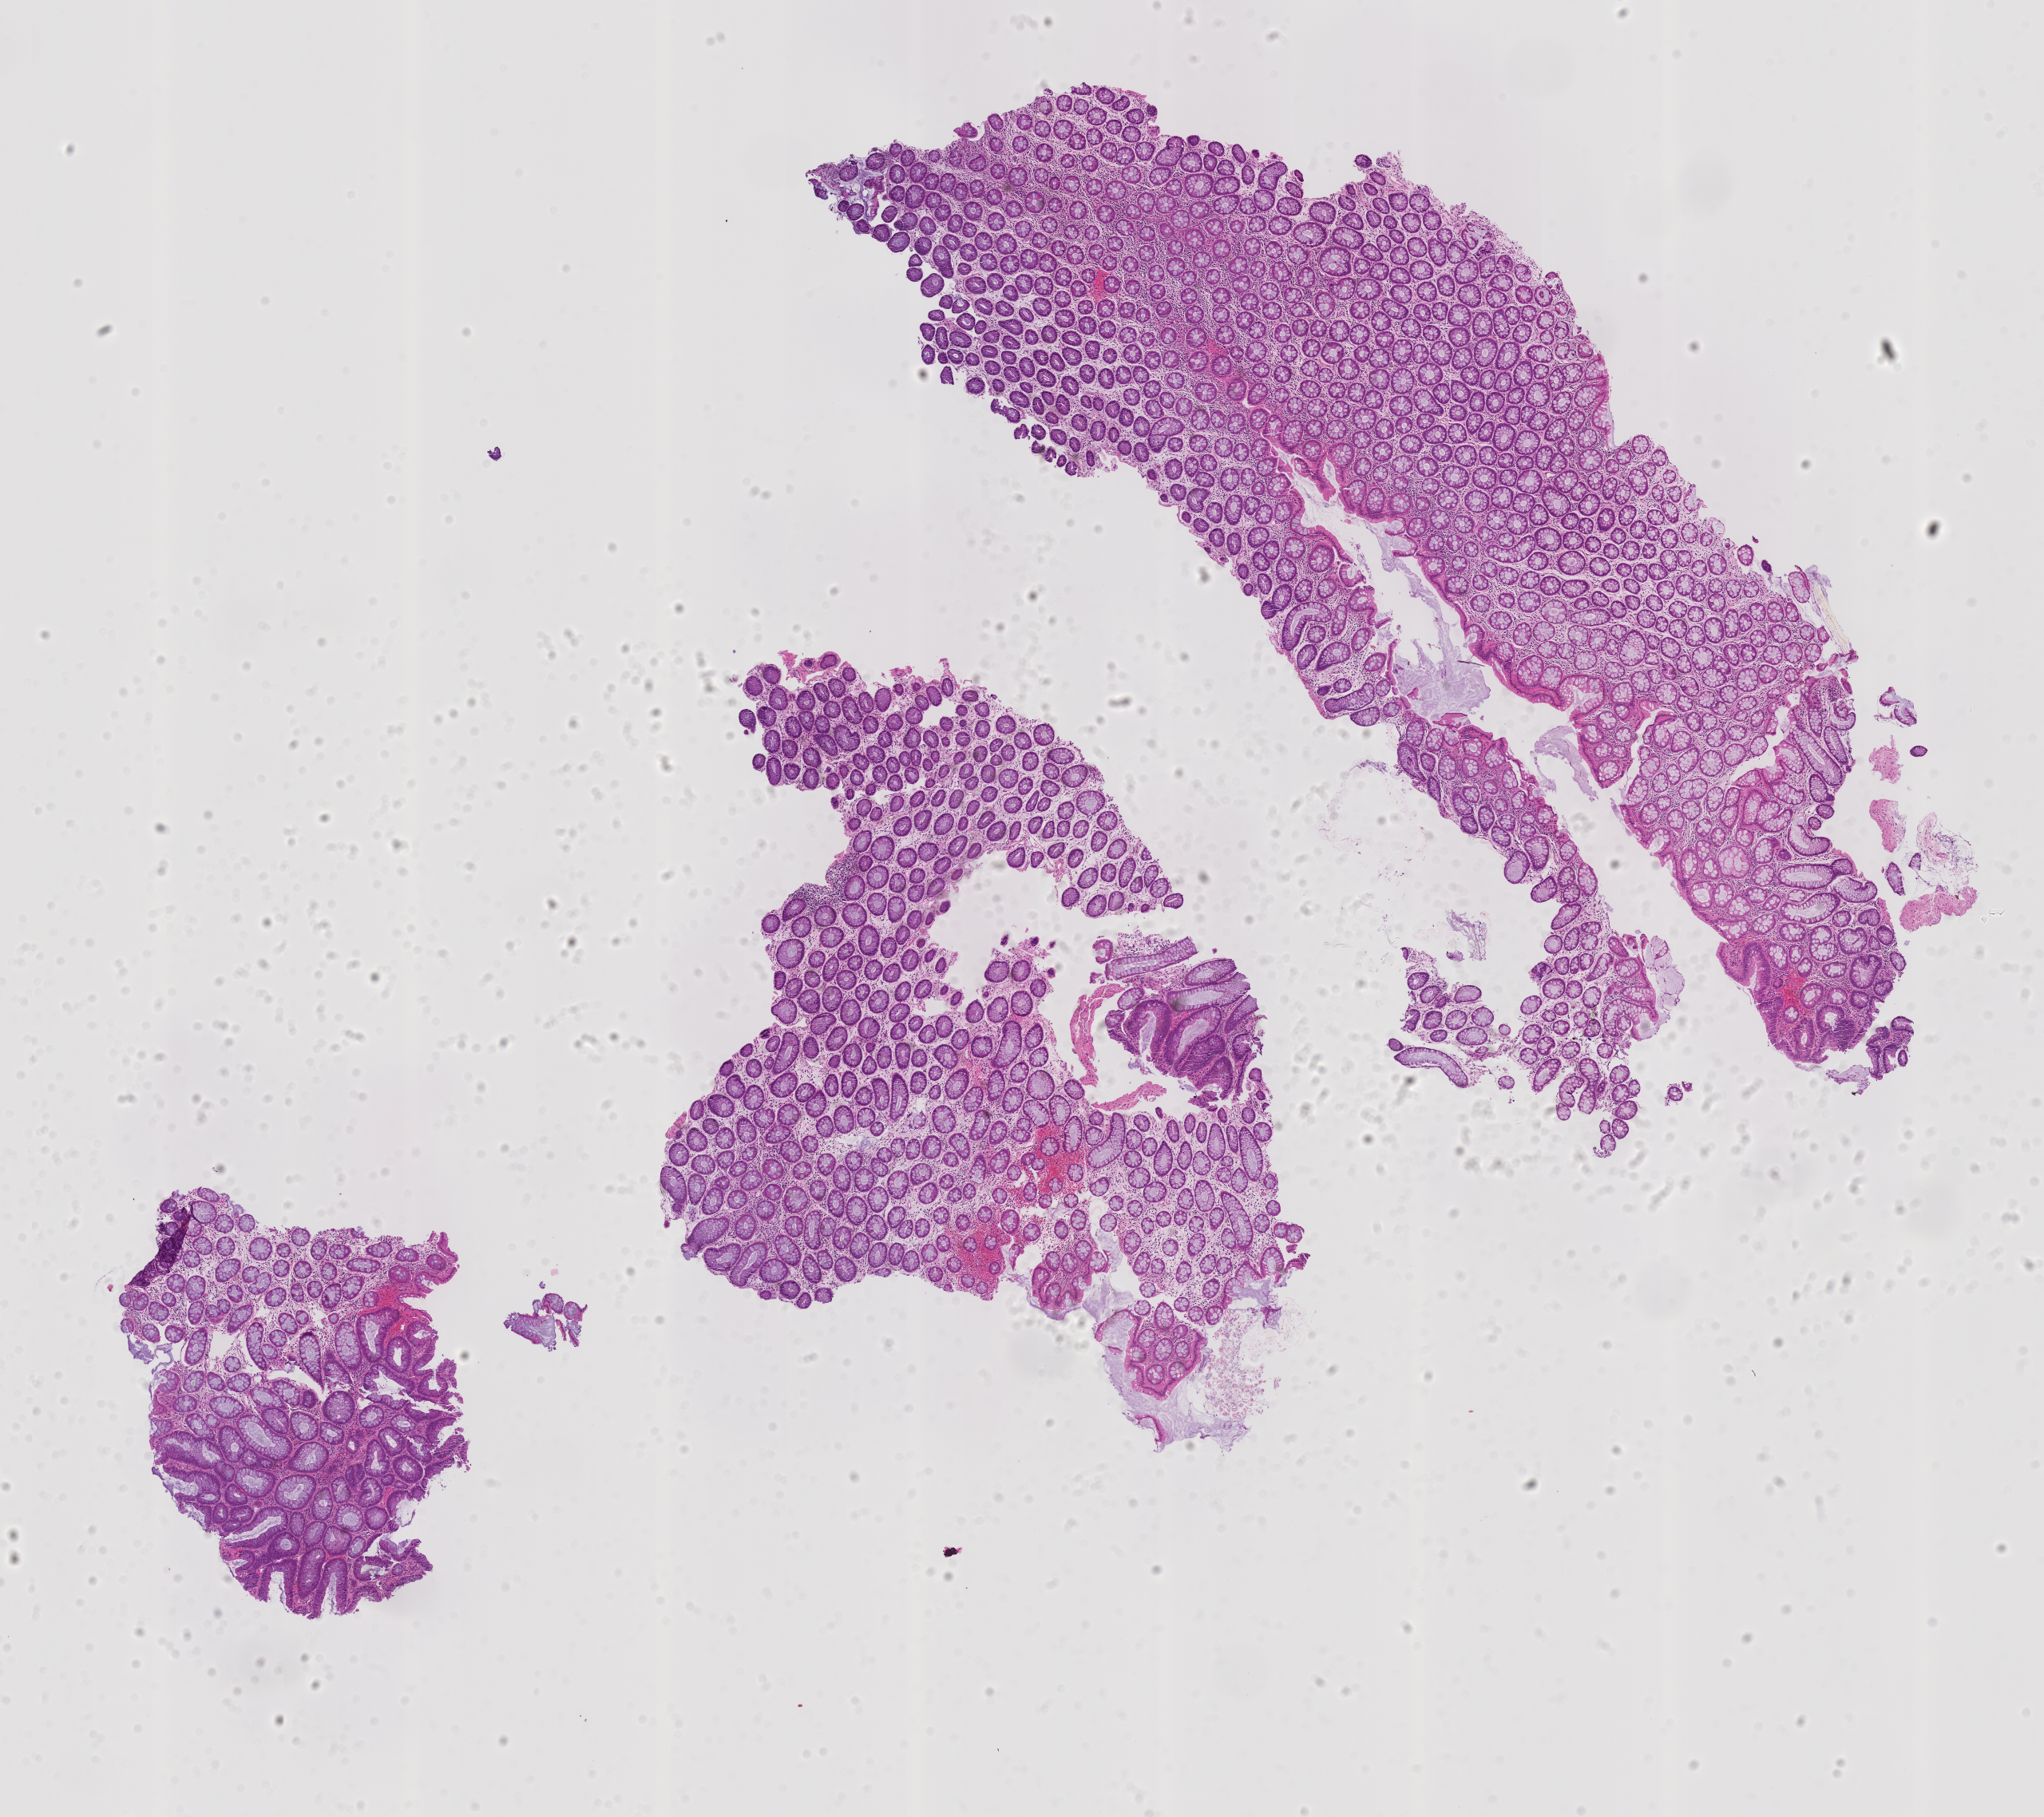
Whole-slide image, hematoxylin and eosin (H&E) stain: colon biopsy — whole scanned area (about 10.2 x 9.1 mm) shown as a low-resolution overview; formalin-fixed, paraffin-embedded (FFPE) tissue; sigmoid colon. Male patient.
Lesion category (as recorded): premalignant.